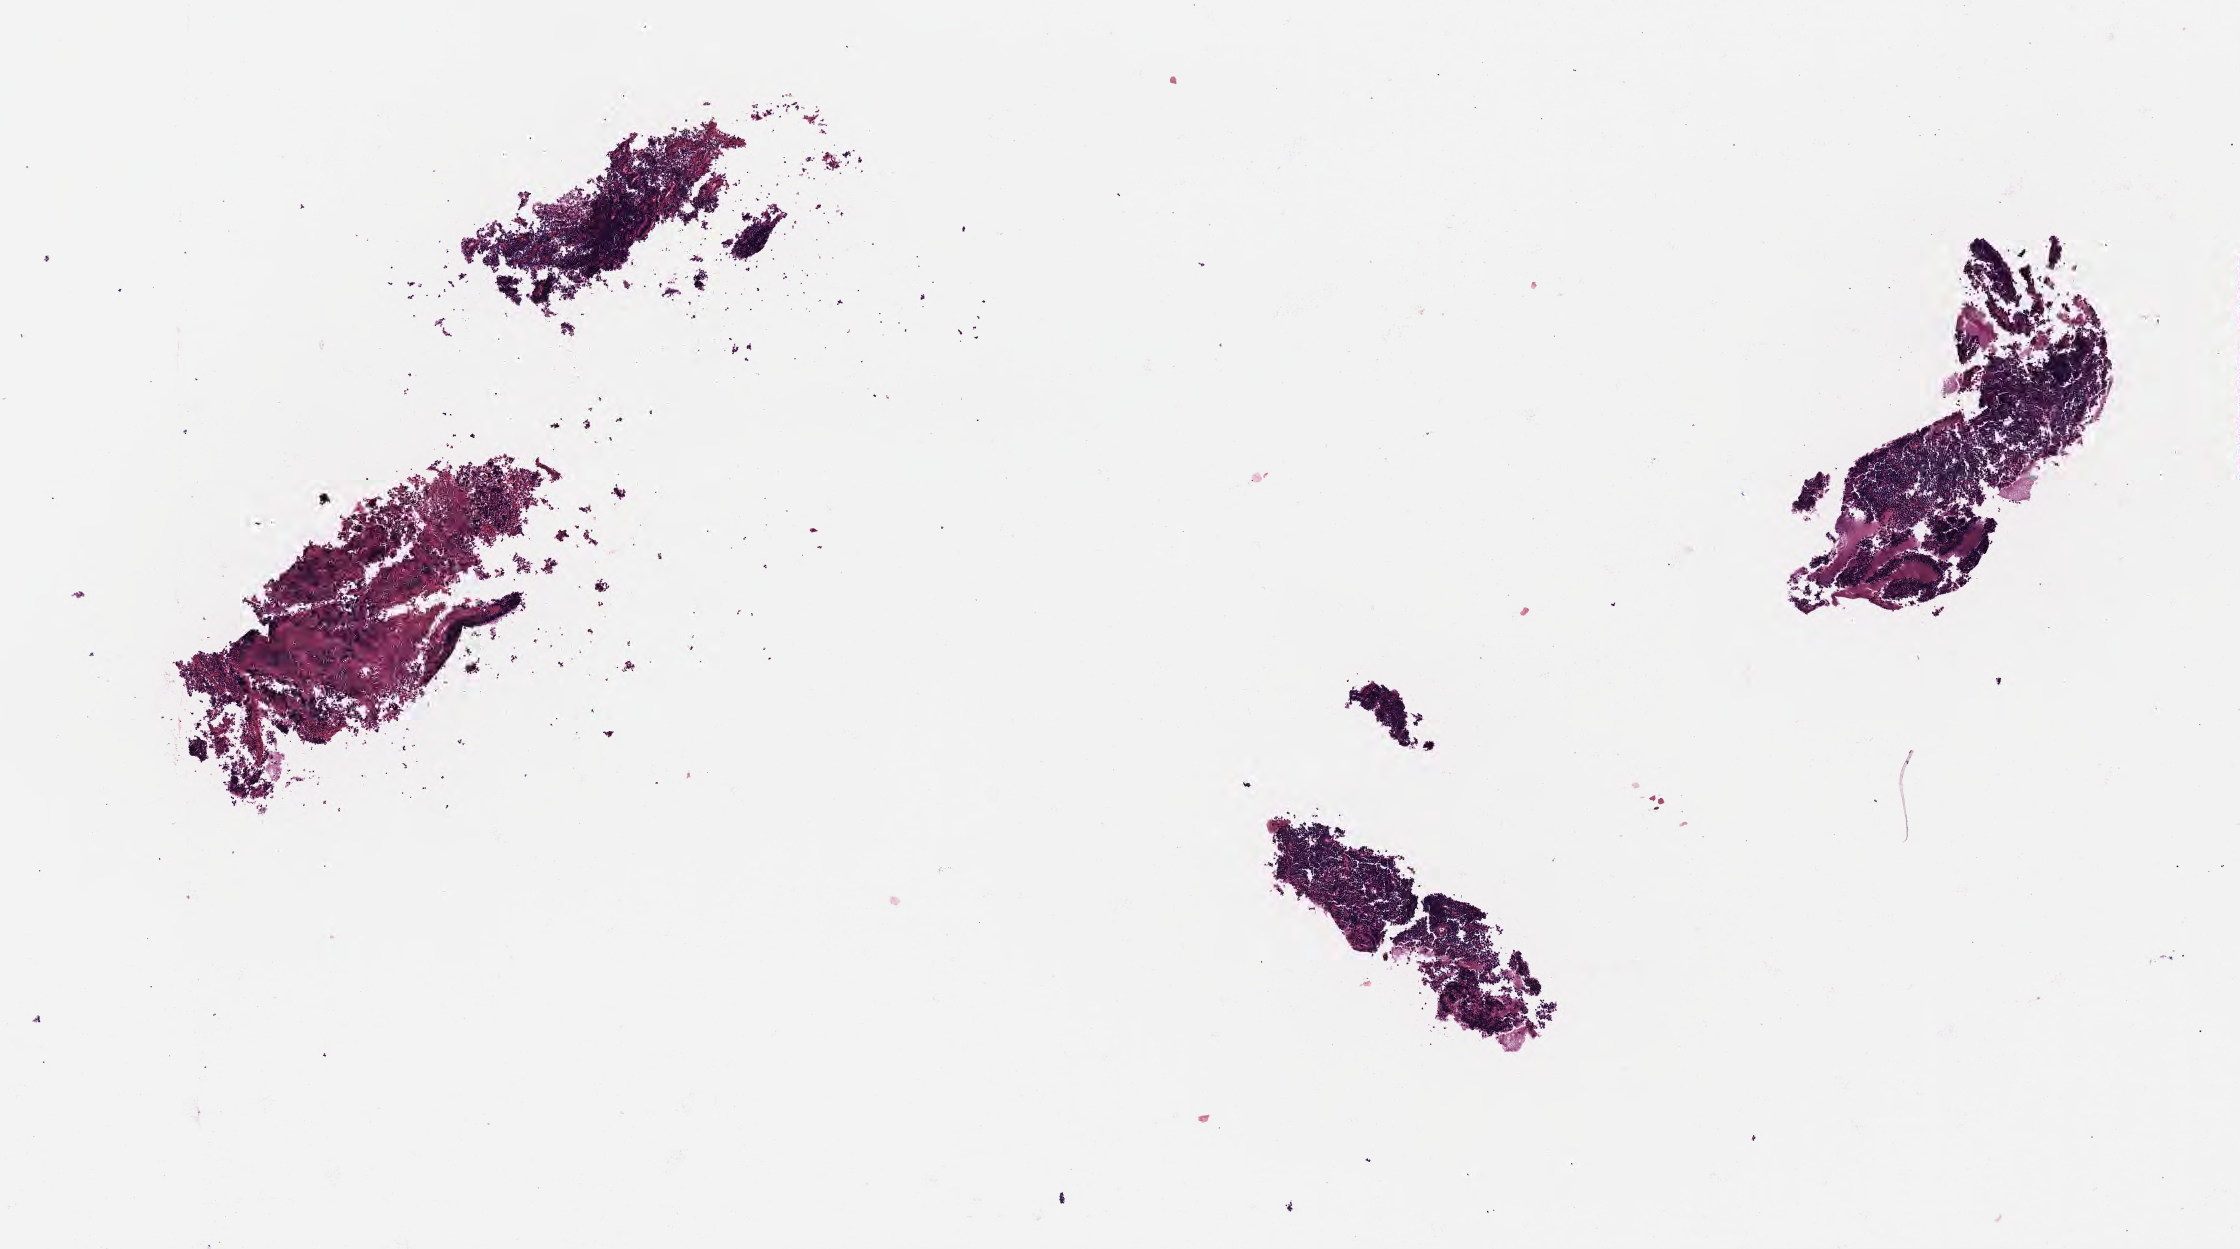
Digitized hematoxylin and eosin (H&E)-stained section, shown as a low-resolution overview of the whole scanned area (about 9.1 x 5.1 mm). Specimen: tumor tissue. Anatomic site: lymph node of head and neck. Patient: female, age at initial diagnosis 4 years.
Histologic diagnosis: Burkitt lymphoma, NOS.